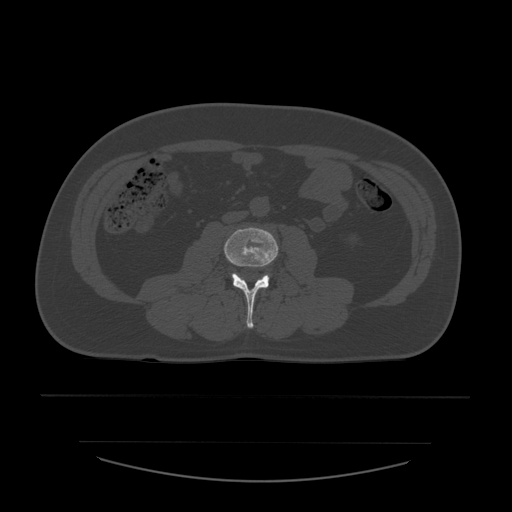
CT including the spine, one axial slice; position 169 of 532 along the scan axis; bone window (W 1800 / L 400 HU); 512 × 512 image matrix, field of view 441 × 441 mm. Patient age 44 years. Case-level facts recorded for this patient, not image findings: primary cancer: soft tissue sarcoma.
Outlined on this slice (semi-automatically segmented with operator editing):
- L3 vertebra: box from (x=224, y=228) to (x=278, y=328) px